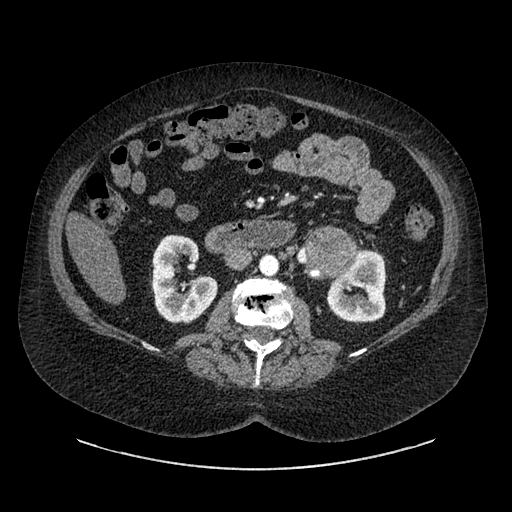
Contrast-enhanced abdominal CT, one axial slice. Position 495 of 769 along the scan axis. Reconstruction kernel SOFT. Intravenous contrast given. Soft-tissue window (W 400 / L 40 HU). 512 × 512 image matrix, field of view 460 × 460 mm. Female patient, age 61 years. From the clinical record (not read from this slice): diagnosis: adrenocortical carcinoma; tumour side: left adrenal; tumour size at pathology: 13 cm; Ki-67 index: 79 %; stage (as recorded): 2.
Structures marked on this image (semi-automatically segmented with operator editing):
- mass: bounding box (x1, y1, x2, y2) in pixels: (312, 232, 354, 274)